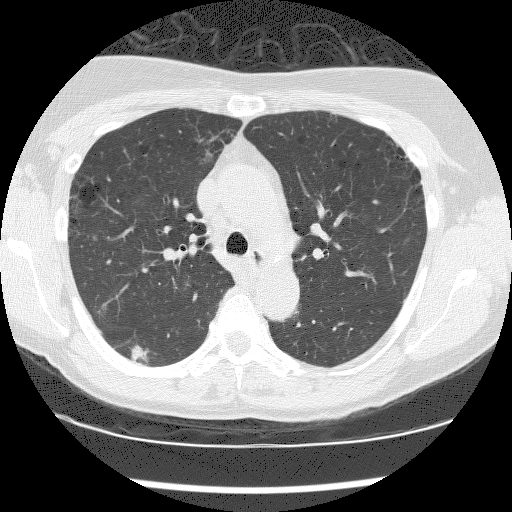
Low-dose screening chest CT, one axial slice. Slice 126 of 176 in the series (ordered by position). Reconstruction kernel BONE. Lung window (W 1500 / L -600 HU). 512 × 512 image matrix, field of view 320 × 320 mm.
Structures marked on this image (expert manual segmentation):
- lesion 1 (tumor, lower lobe of right lung): box from (x=131, y=345) to (x=149, y=362) px